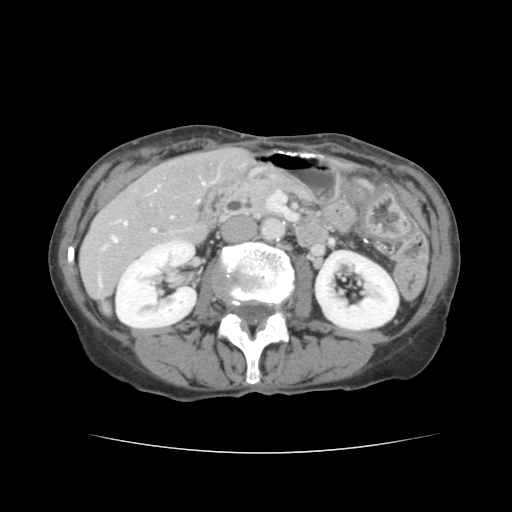
Contrast-enhanced abdominal CT, one axial slice. Position 56 of 136 along the scan axis. Soft-tissue window (W 400 / L 40 HU). 2.5 mm slice thickness. 512 × 512 image matrix, field of view 319 × 319 mm. Female patient, age 77 years. From the clinical record (not read from this slice): diagnosis: colorectal cancer liver metastases, imaged before liver resection.
Outlined on this slice (expert manual segmentation):
- hepatic veins: bounding box (x1, y1, x2, y2) in pixels: (112, 182, 205, 242)
- liver: (81, 147, 250, 305)
- planned liver remnant (the part of the liver to remain after resection): (166, 147, 250, 196)
- portal vein (with intrahepatic branches): (99, 228, 156, 286)